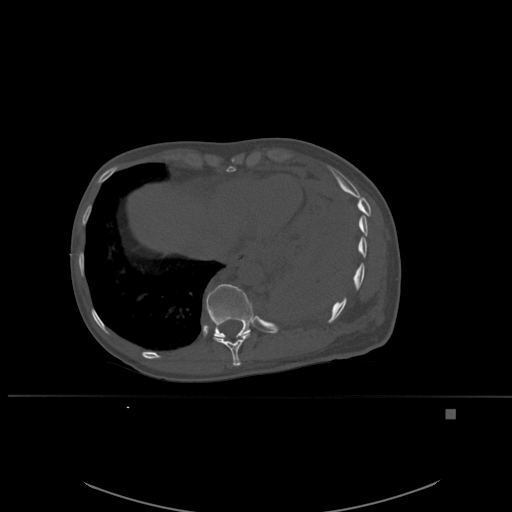
CT including the spine, one axial slice. Bone window (W 1800 / L 400 HU). 1.5 mm slice thickness. 512 × 512 image matrix. Patient: female, 45 years. Case-level facts recorded for this patient, not image findings: primary cancer: lung.
Outlined on this slice (semi-automatically segmented with operator editing):
- T10 vertebra: box from (x=213, y=331) to (x=251, y=366) px
- T11 vertebra: (x=206, y=284)–(x=254, y=338)